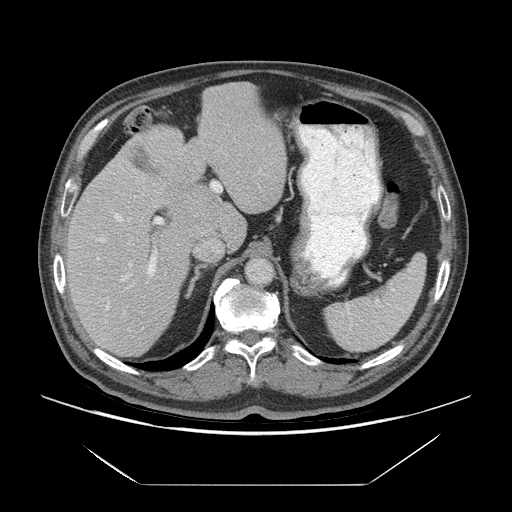
Contrast-enhanced abdominal CT (liver protocol), one axial slice. Reconstruction kernel STANDARD. Soft-tissue window (W 400 / L 40 HU). 2.5 mm slice thickness. 512 × 512 image matrix, field of view 420 × 420 mm. Case-level facts recorded for this patient, not image findings: diagnosis: hepatocellular carcinoma (patient treated with transarterial chemoembolisation; whether this scan precedes or follows treatment is not stated here); TNM stage (as recorded): Stage-I; Child-Pugh class: A; tumour differentiation: well differentiated; tumour nodularity: uninodular.
Outlined on this slice (semi-automatically segmented with operator editing):
- liver parenchyma outside the tumour (the mass and vessels are separate outlines, so this box may not span the whole liver): bounding box (x1, y1, x2, y2) in pixels: (66, 82, 286, 356)
- mass: (170, 186, 223, 234)
- liver vessels: (97, 213, 164, 311)